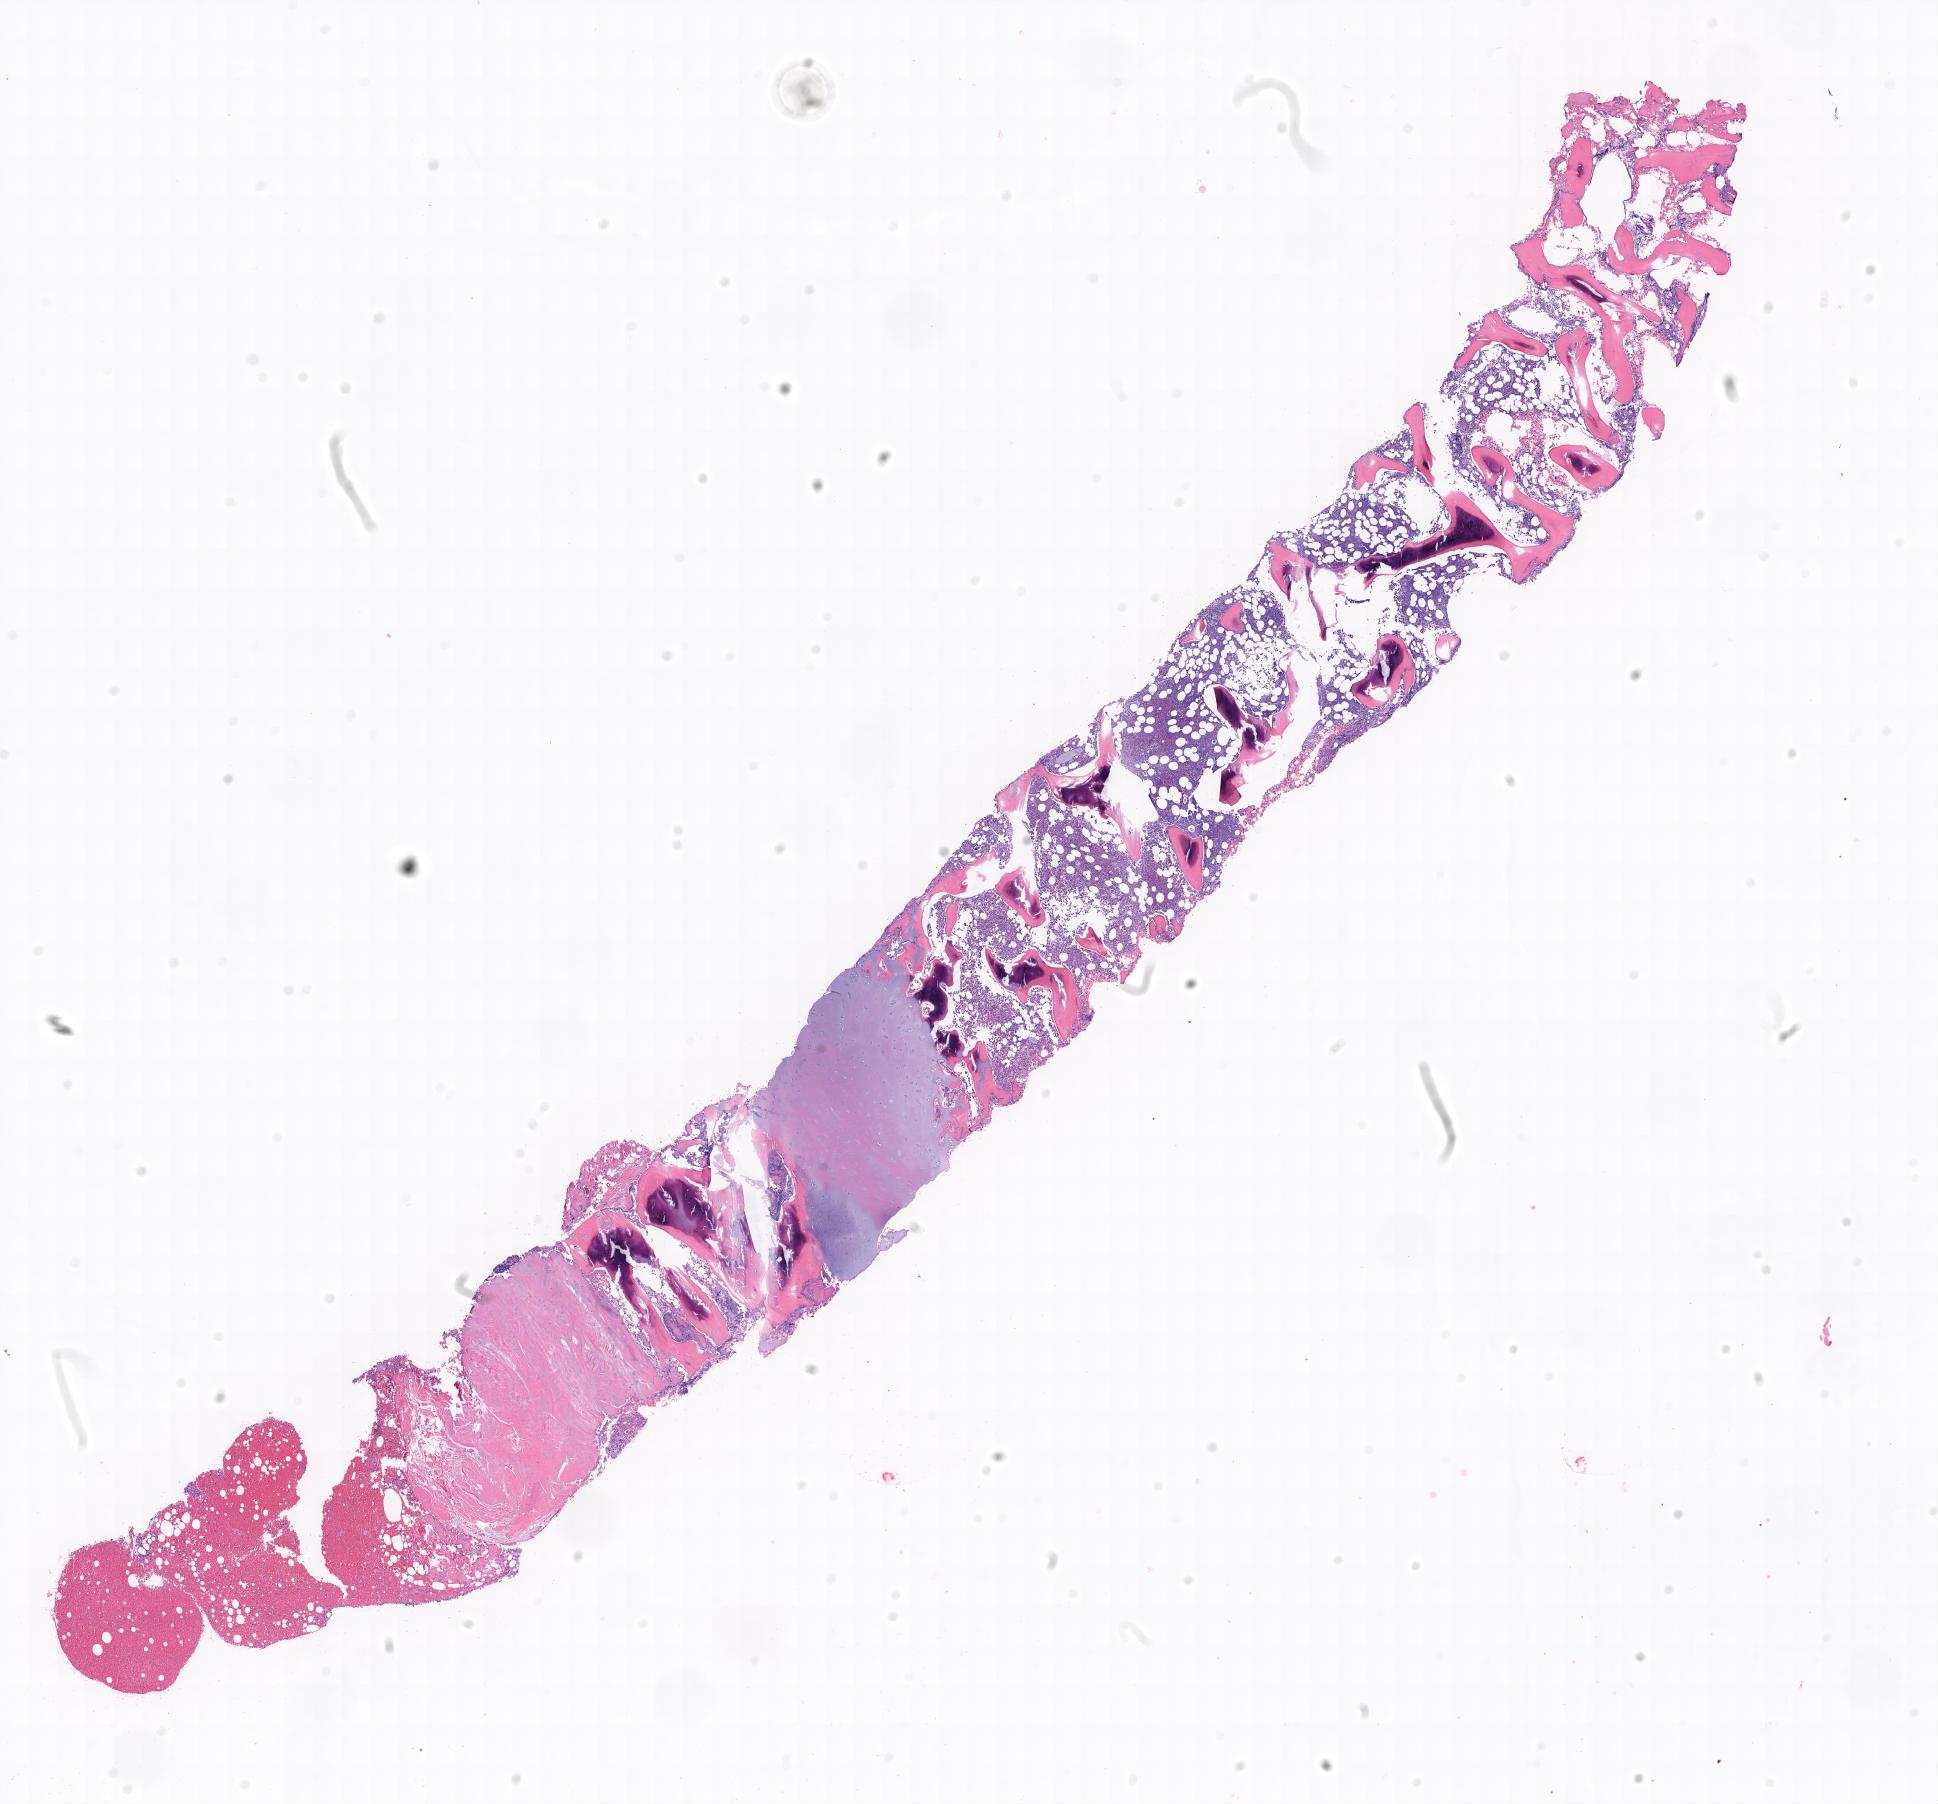
Digitized haematoxylin and eosin-stained section — a low-resolution overview of the entire scanned area, specimen: tumor tissue, site: bone marrow. Patient male; age 15 years.
Diagnosis: Burkitt lymphoma, NOS.